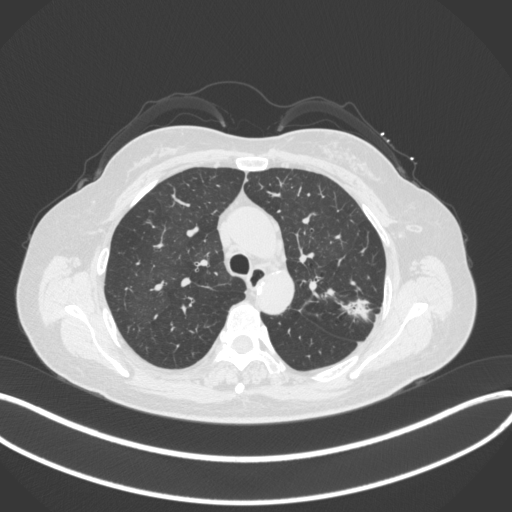
Chest CT, one axial slice. Reconstruction kernel B31f. Lung window (W 1500 / L -600 HU). 1 mm slice thickness. 512 × 512 image matrix. Female patient, age 60 years. From the clinical record (not read from this slice): clinical TNM (as recorded): T1c N0 M0.
Annotated regions visible in this slice (rectangle marked by the reading radiologist):
- lung tumour (recorded histology: adenocarcinoma): box from (x=337, y=296) to (x=374, y=325) px